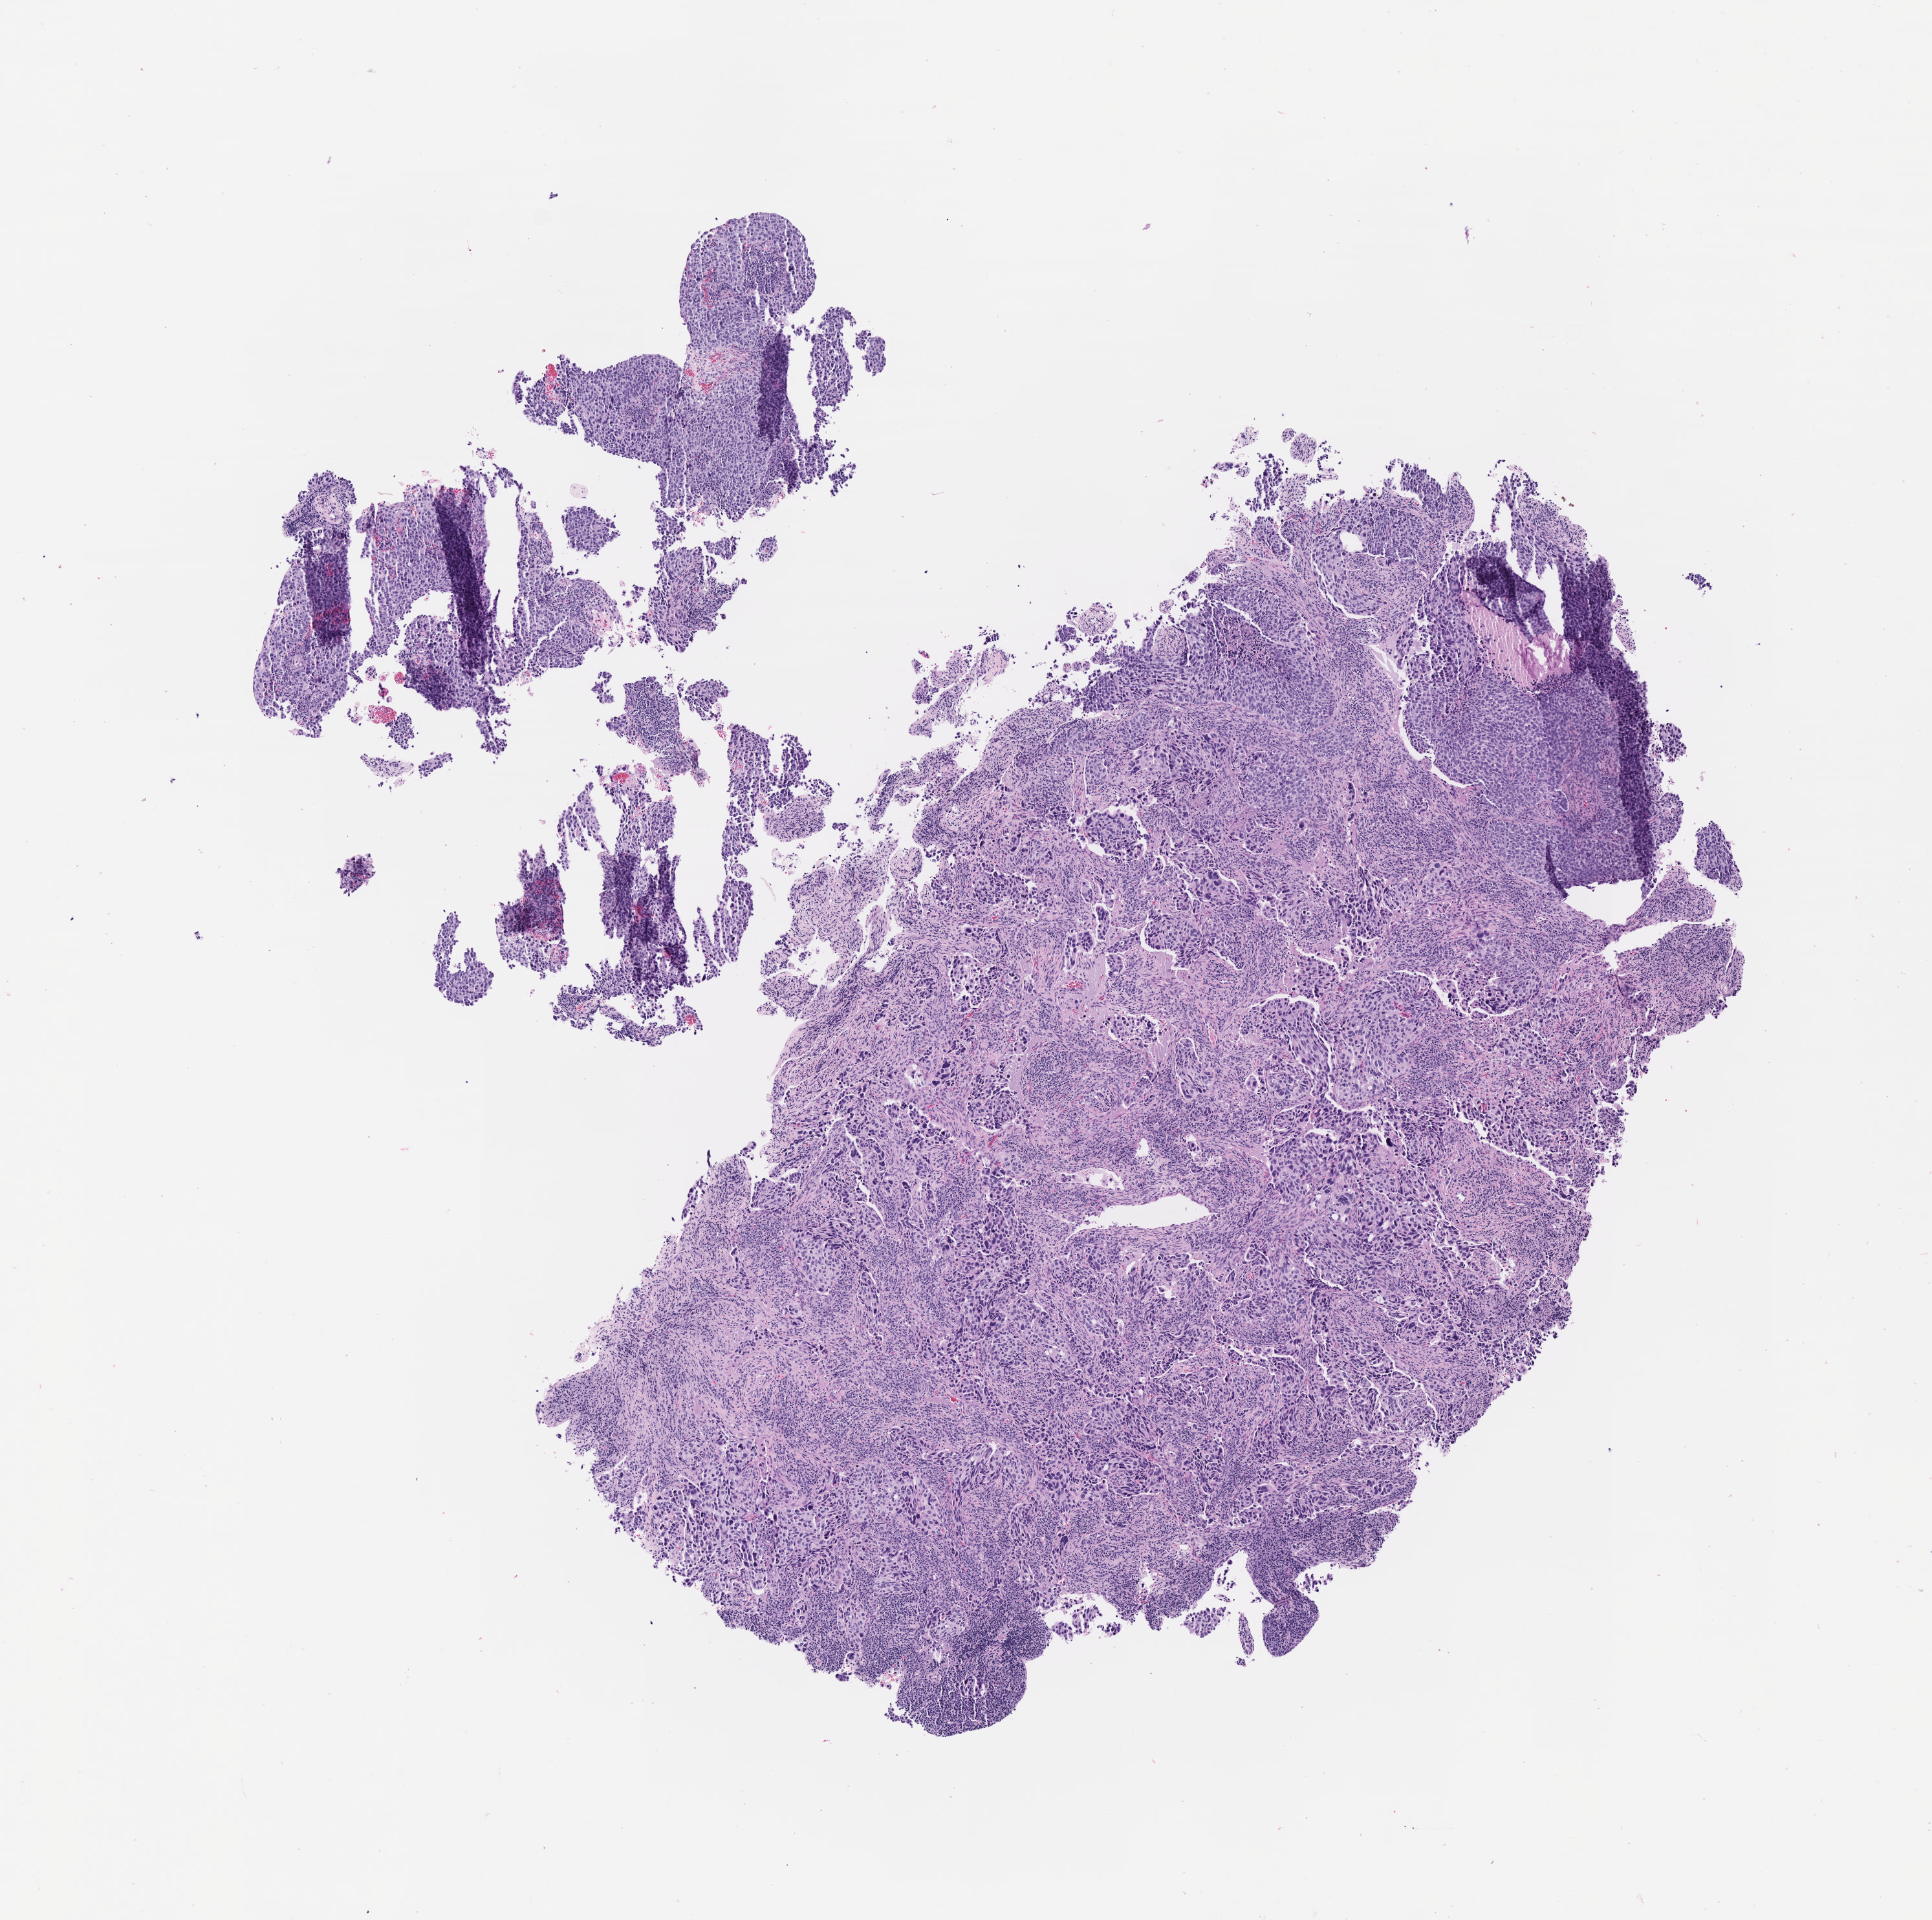
Digitized H&E-stained section — whole scanned area (about 6.0 x 6.0 mm) shown as a low-resolution overview, tumor tissue, anatomic site: cervix. Patient: female, aged 47.
Diagnosis: Squamous cell carcinoma, large cell, nonkeratinizing, NOS.